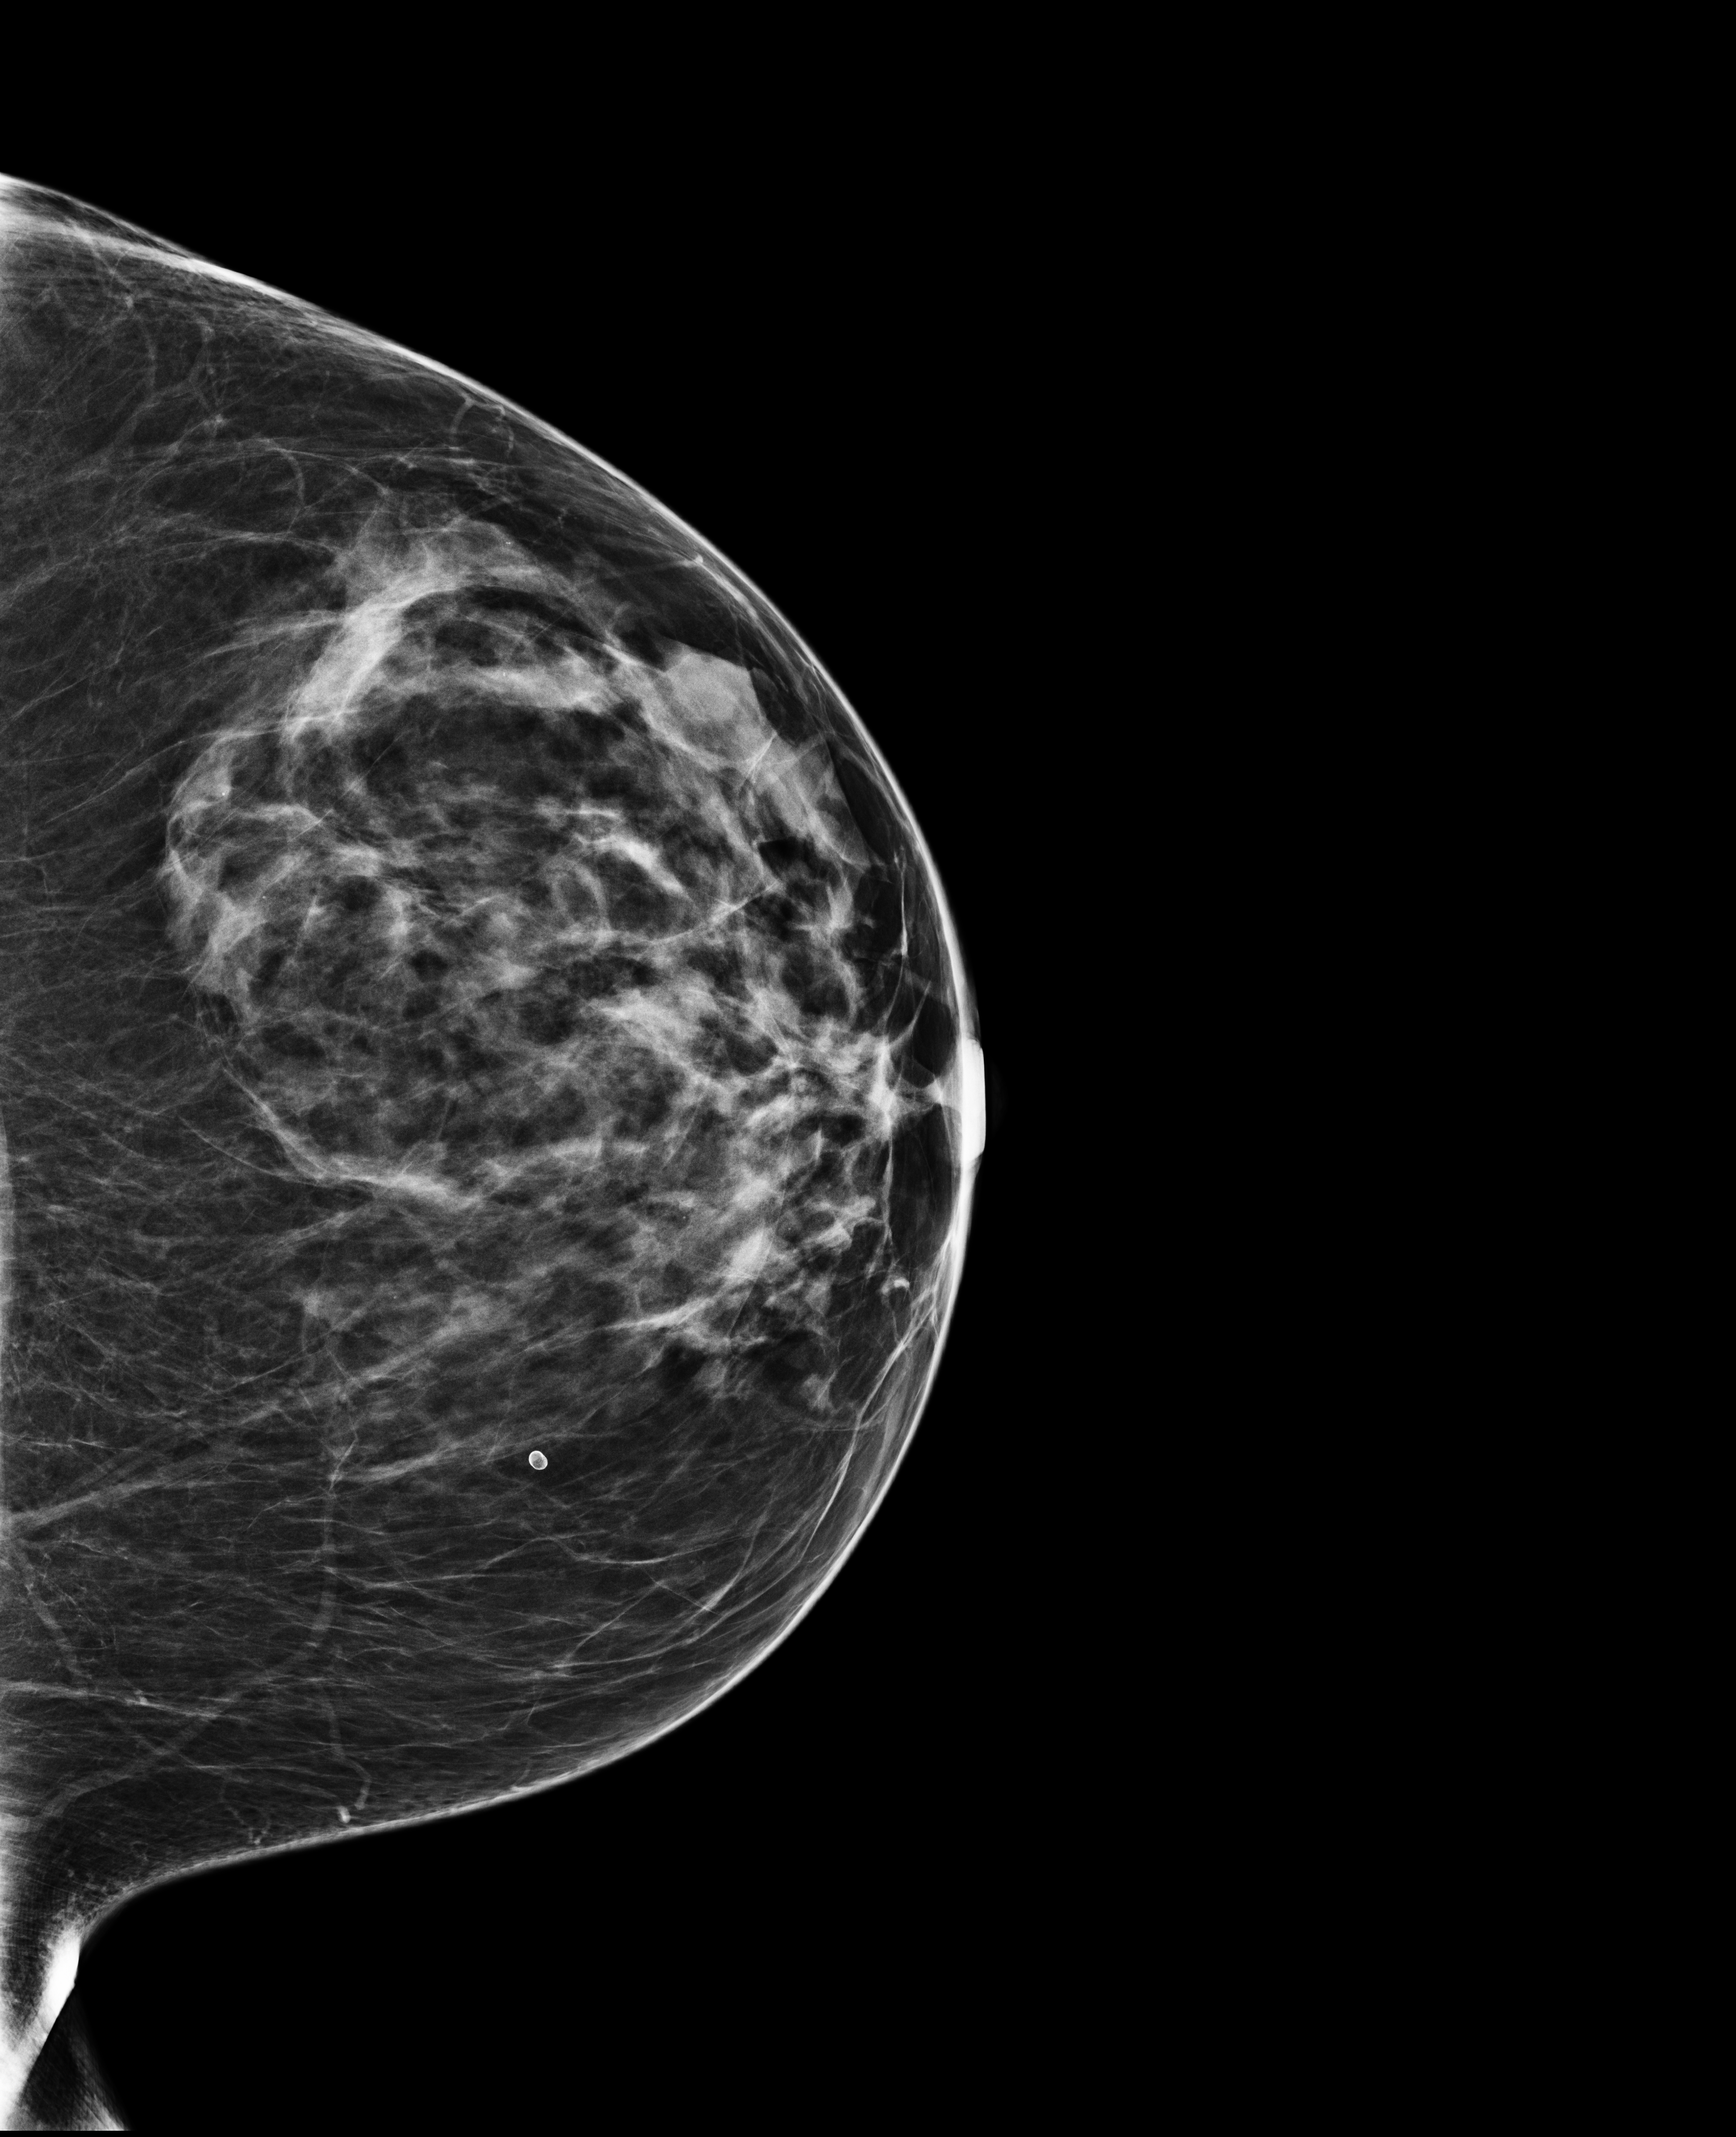
Full-field digital mammogram (FFDM), left breast, CC view, screening examination, compressed breast thickness 69 mm. Patient aged 57 years (female).
Breast density at the screening exam (both breasts): heterogeneously dense (BI-RADS density category c). Final BI-RADS assessment for this screening round (tomosynthesis exam, both breasts): category 1. Recall: no recall after this screen.